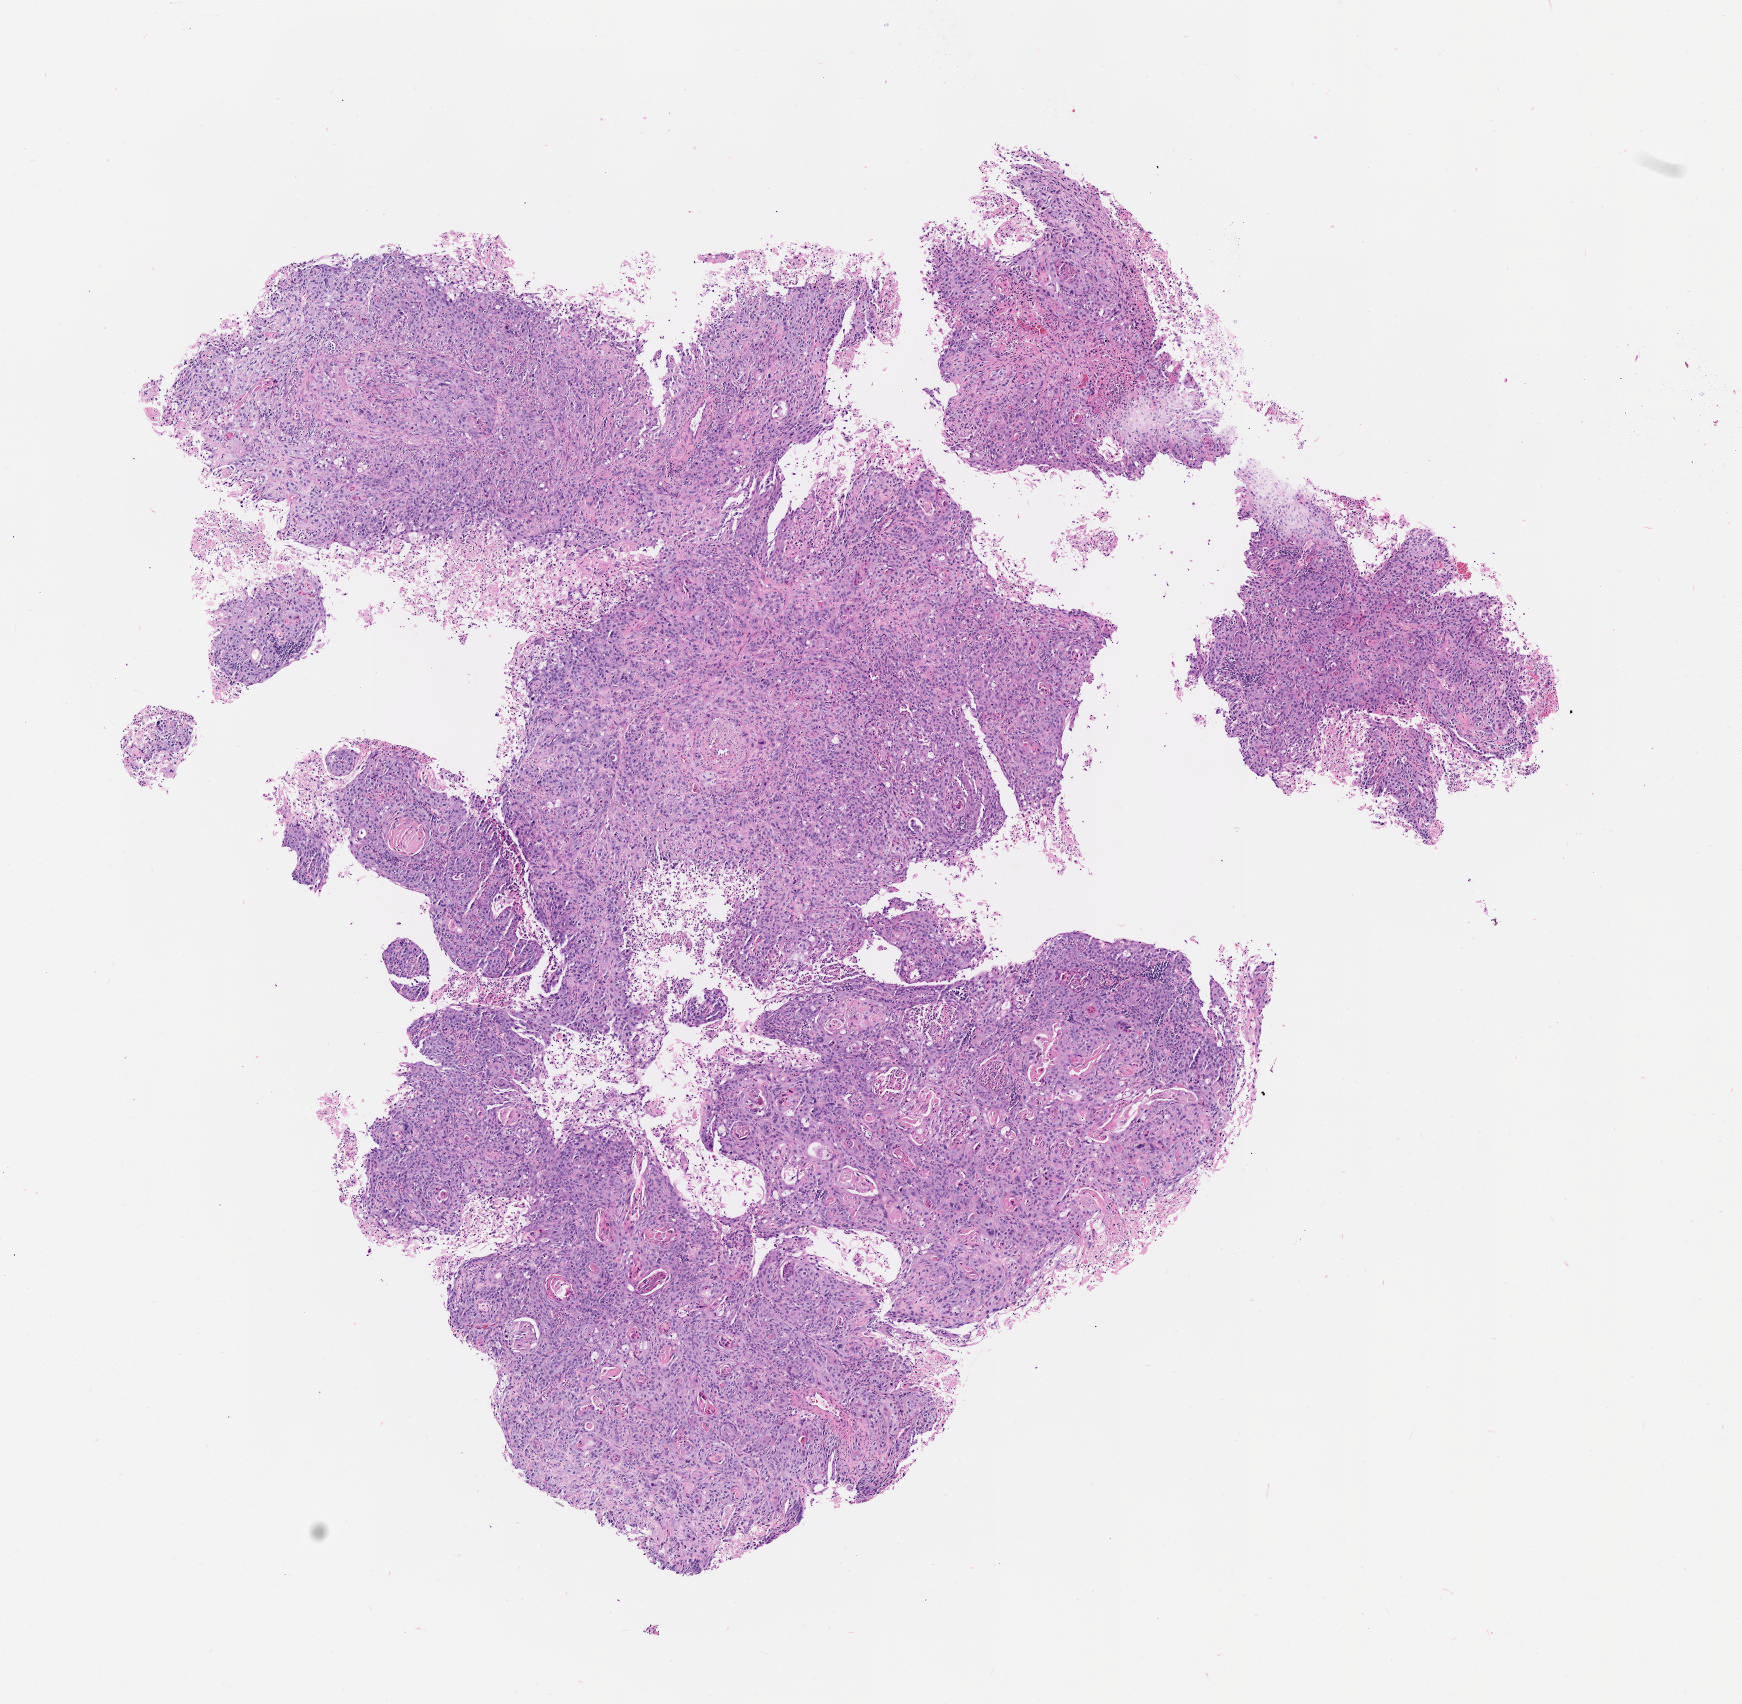
Digitized haematoxylin and eosin-stained section, whole scanned area (about 7.0 x 6.9 mm) shown as a low-resolution overview. Specimen: tumor tissue. Anatomic site: cervix. Patient: female, 33 years old.
Histologic diagnosis: Squamous cell carcinoma, keratinizing, NOS.